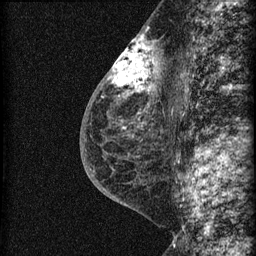
Breast MRI (dynamic contrast-enhanced), one sagittal slice. Dynamic contrast-enhanced series, image 2 of 3 at this slice position (ordered by acquisition). 1.5 T. TE 4.2 ms, TR 22.7 ms. 1.5 mm slice thickness. 256 × 256 image matrix, field of view 180 × 180 mm. Female patient, age 48 years. From the clinical record (not read from this slice): setting: breast cancer imaged before/during neoadjuvant chemotherapy; receptor status: triple-negative.
Outlined on this slice (semi-automatically segmented with operator editing):
- analysis volume of interest (the breast-tissue region the enhancement analysis was run in; not a lesion): box from (x=115, y=34) to (x=169, y=162) px
- tumour enhancement mask (voxels above the 90 % enhancement threshold inside the analysis volume of interest): (x=115, y=35)–(x=158, y=92)